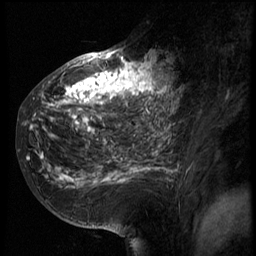
Breast MRI (dynamic contrast-enhanced), one sagittal slice; slice 31 of 66 in the series (ordered by position); 3 images stored at this slice position (order not interpretable as contrast timing); 1.5 T; TE 4.2 ms, TR 8.9 ms; 2.5 mm slice thickness; 256 × 256 image matrix. Patient: female, 39 years. Case-level facts recorded for this patient, not image findings: setting: breast cancer imaged before/during neoadjuvant chemotherapy; receptor status: HER2-positive.
Structures marked on this image (semi-automatic segmentation, software-assisted and operator-edited):
- analysis volume of interest (the breast-tissue region the enhancement analysis was run in; not a lesion): box from (x=29, y=44) to (x=166, y=196) px
- tumour enhancement mask (voxels above the 140 % enhancement threshold inside the analysis volume of interest): (x=29, y=51)–(x=166, y=188)